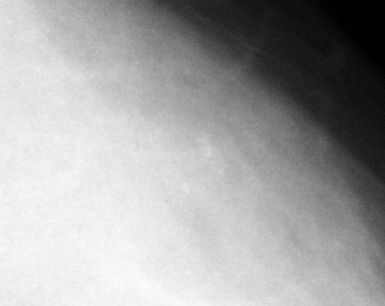
Cropped region of a digitized screen-film mammogram centred on a radiologist-marked abnormality, left breast, CC view, BI-RADS breast density category 4 (scale 1–4).
Calcifications, morphology amorphous, distribution clustered; BI-RADS assessment category 4; subtlety rating 3 on a 1 (subtle) to 5 (obvious) scale; pathology result (as recorded, not read from the image): benign.